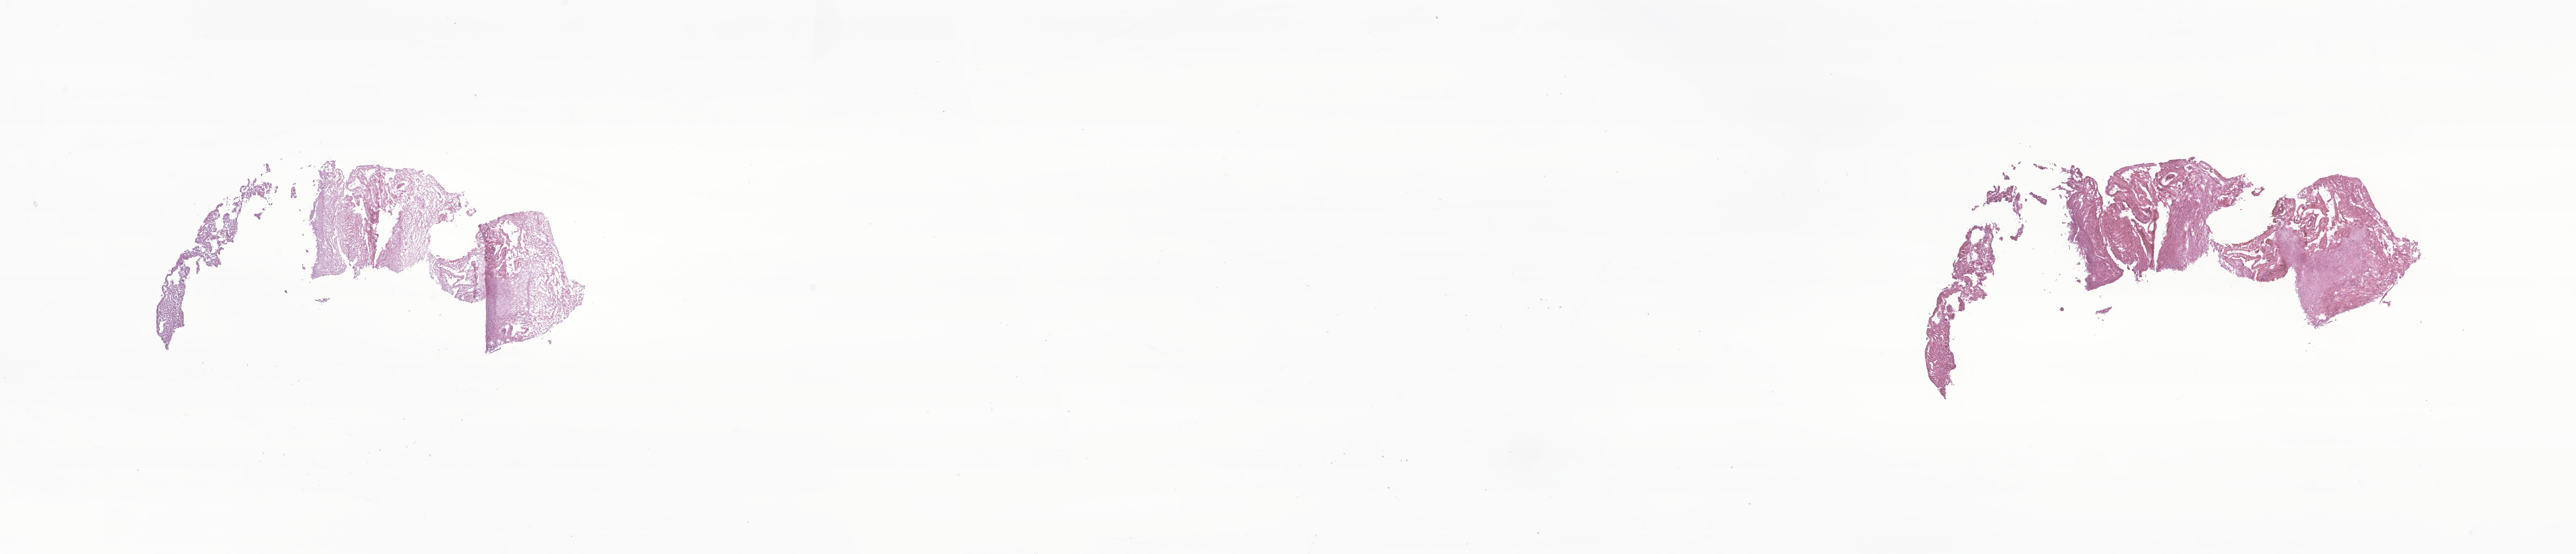
Digitized haematoxylin and eosin-stained section of tumor tissue from the brain — whole scanned area (about 32.0 x 6.9 mm) shown as a low-resolution overview, cryosection (OCT / tissue freezing medium). Patient: male, age 172 months.
Diagnosis: Pilocytic astrocytoma.